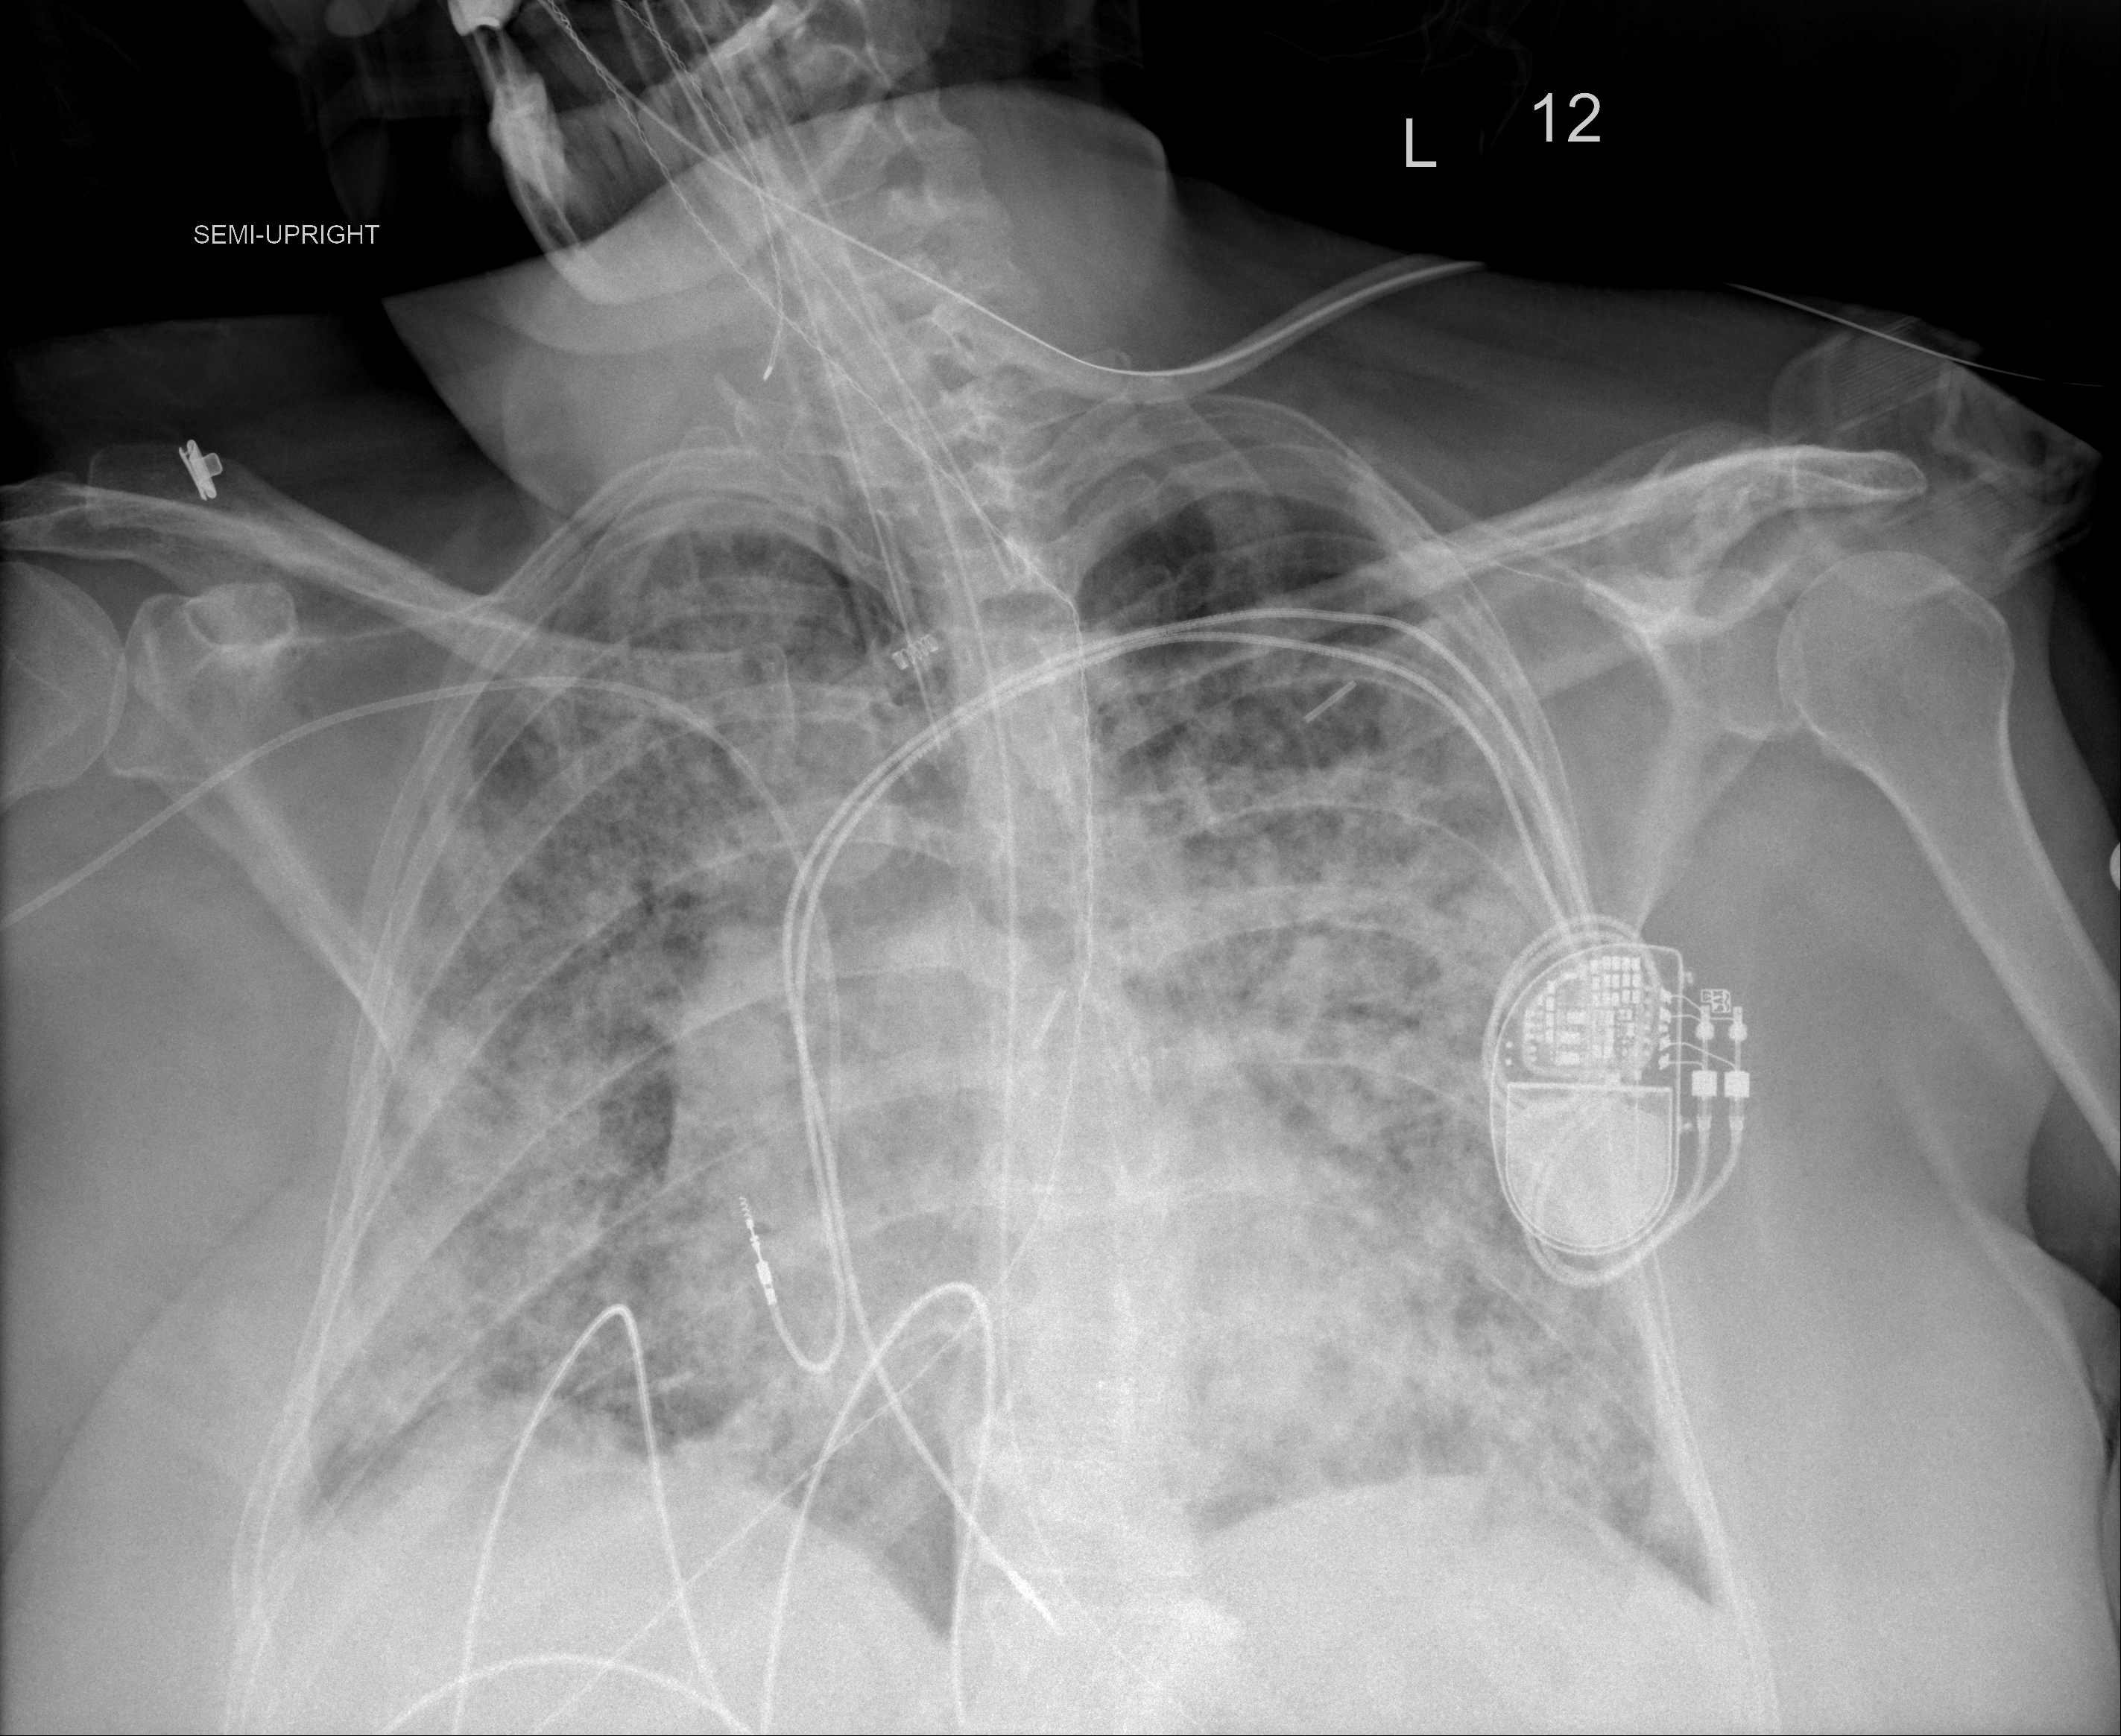
Chest X-ray (portable), AP projection. Female patient, age 57 years; COVID-19 (test-positive).
Radiologist key findings (as recorded): Extensive airspace disease throughout the lungs shows no improvement.